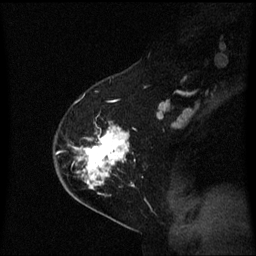
Breast MRI (dynamic contrast-enhanced), one sagittal slice. Slice 40 of 60 in the series (ordered by position). Dynamic contrast-enhanced series, image 2 of 3 at this slice position (ordered by acquisition). 1.5 T. TE 4.2 ms, TR 8.4 ms. 256 × 256 image matrix, field of view 210 × 210 mm. Patient: female, 54 years. Case-level facts recorded for this patient, not image findings: setting: breast cancer imaged before/during neoadjuvant chemotherapy; receptor status: HER2-positive.
Annotated regions visible in this slice (semi-automatically segmented with operator editing):
- analysis volume of interest (the breast-tissue region the enhancement analysis was run in; not a lesion): bounding box [x1, y1, x2, y2] px = [59, 126, 136, 199]
- tumour enhancement mask (voxels above the 70 % enhancement threshold inside the analysis volume of interest): [79, 127, 130, 190]